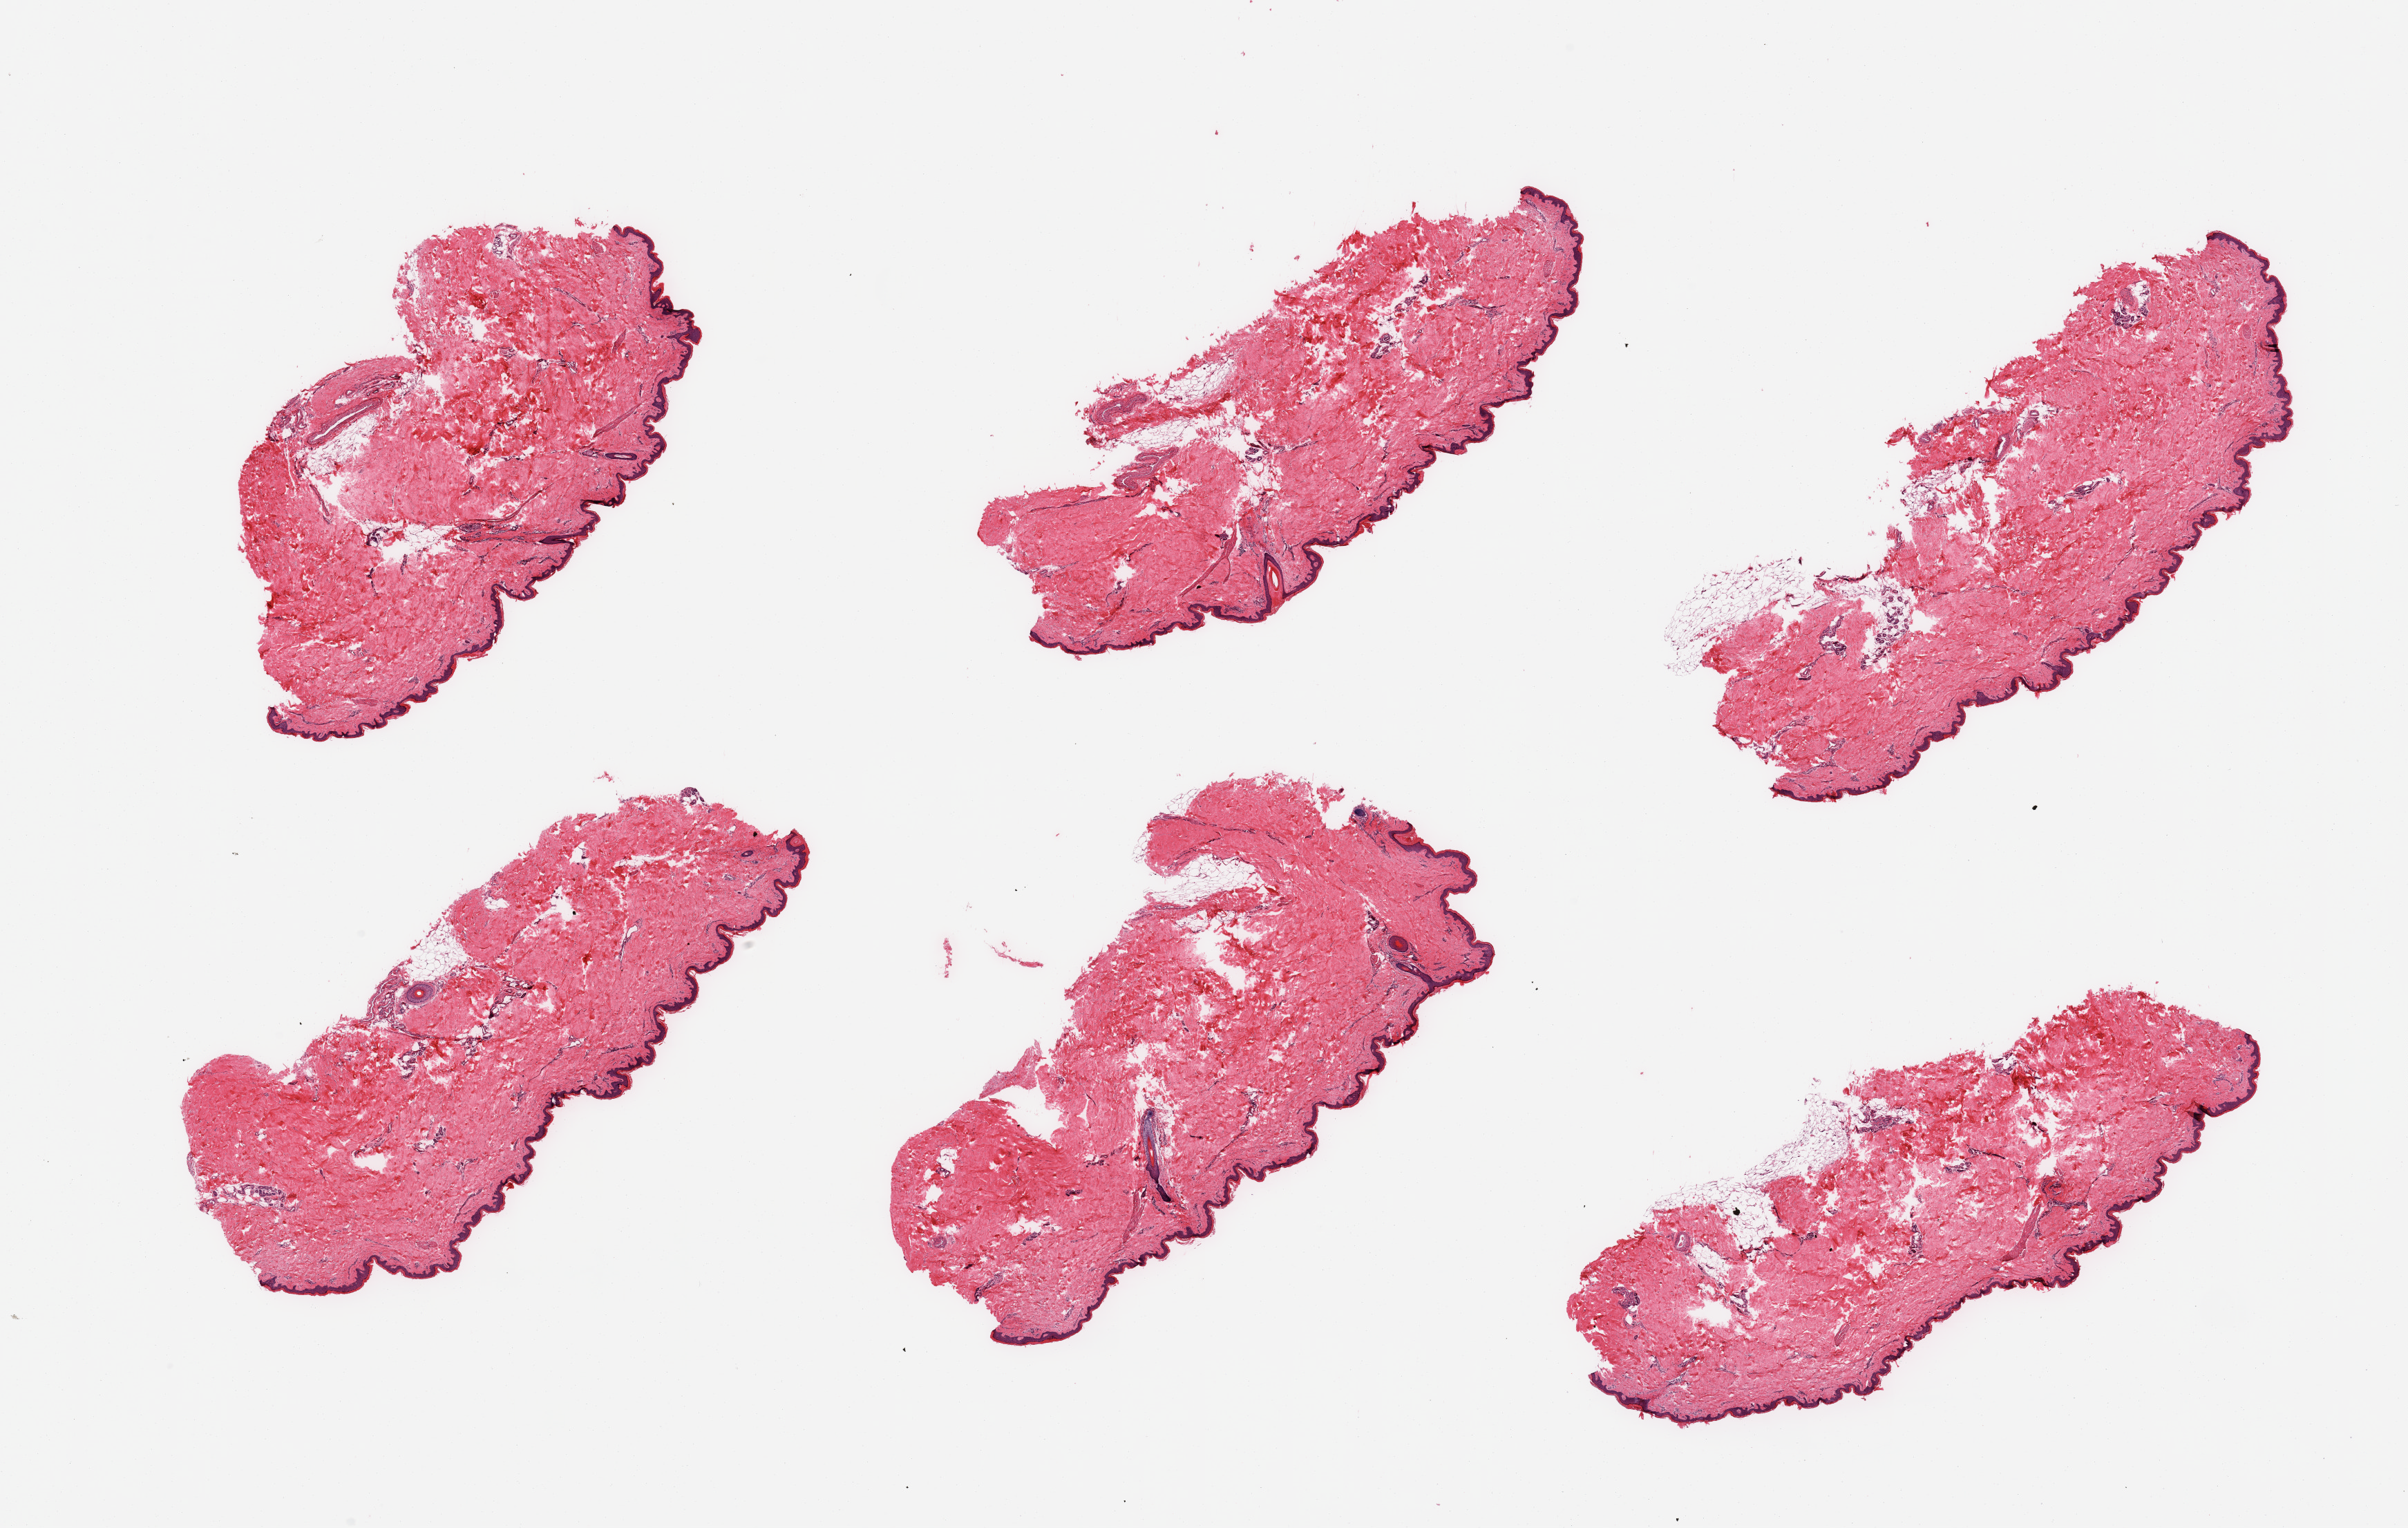
H&E whole-slide image, whole scanned area (about 27.6 x 17.5 mm, acquisition: 20x scan) shown as a low-resolution overview; PAXgene-fixed paraffin-embedded (PFPE) section; sampled site (target tissue): skin of lower leg; tissue donor sample.
- pathologist's review note for this sample: 6 pieces, no dermal fat, squamous epithelium is 25-50 microns